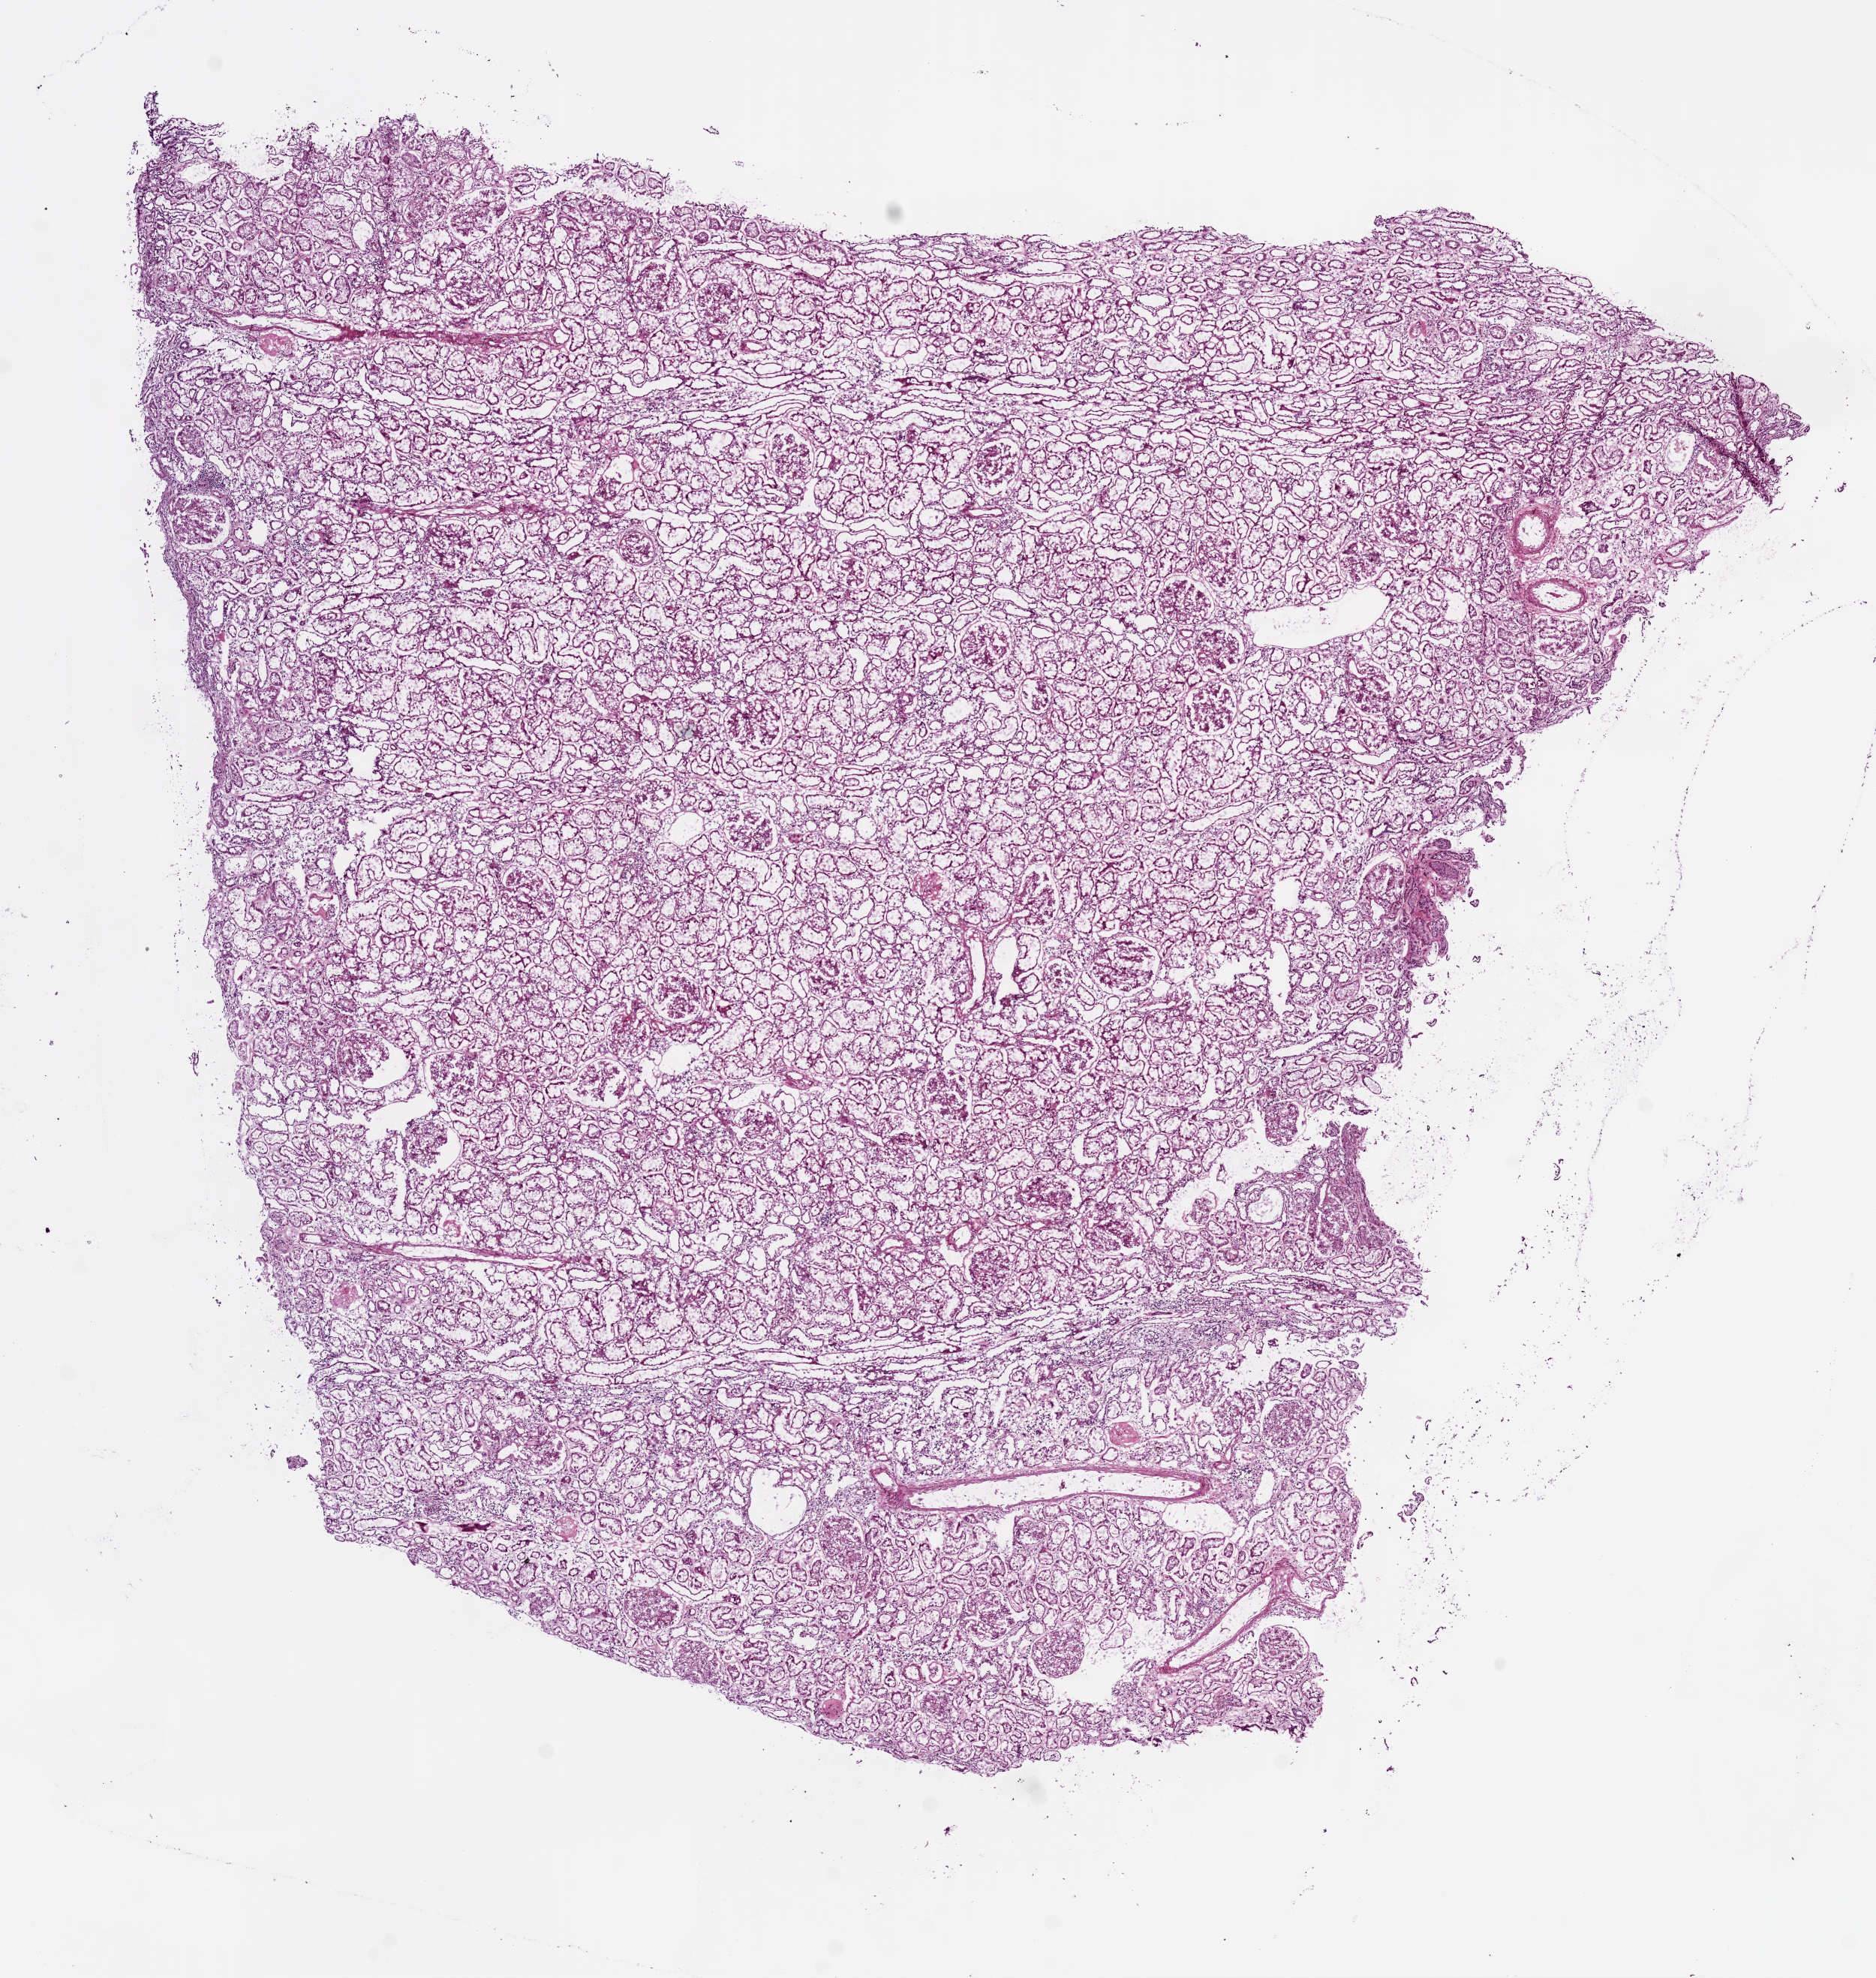
Whole-slide histology image, H&E-stained, whole scanned area (about 10.0 x 10.6 mm) shown as a low-resolution overview. Frozen section from the bottom of the tissue portion. Kidney, solid tissue normal (non-tumour tissue) sample. Male patient; age at initial diagnosis 54 years.
* this section: solid tissue normal sample (biorepository sample class)
* patient diagnosis: Clear cell adenocarcinoma, NOS